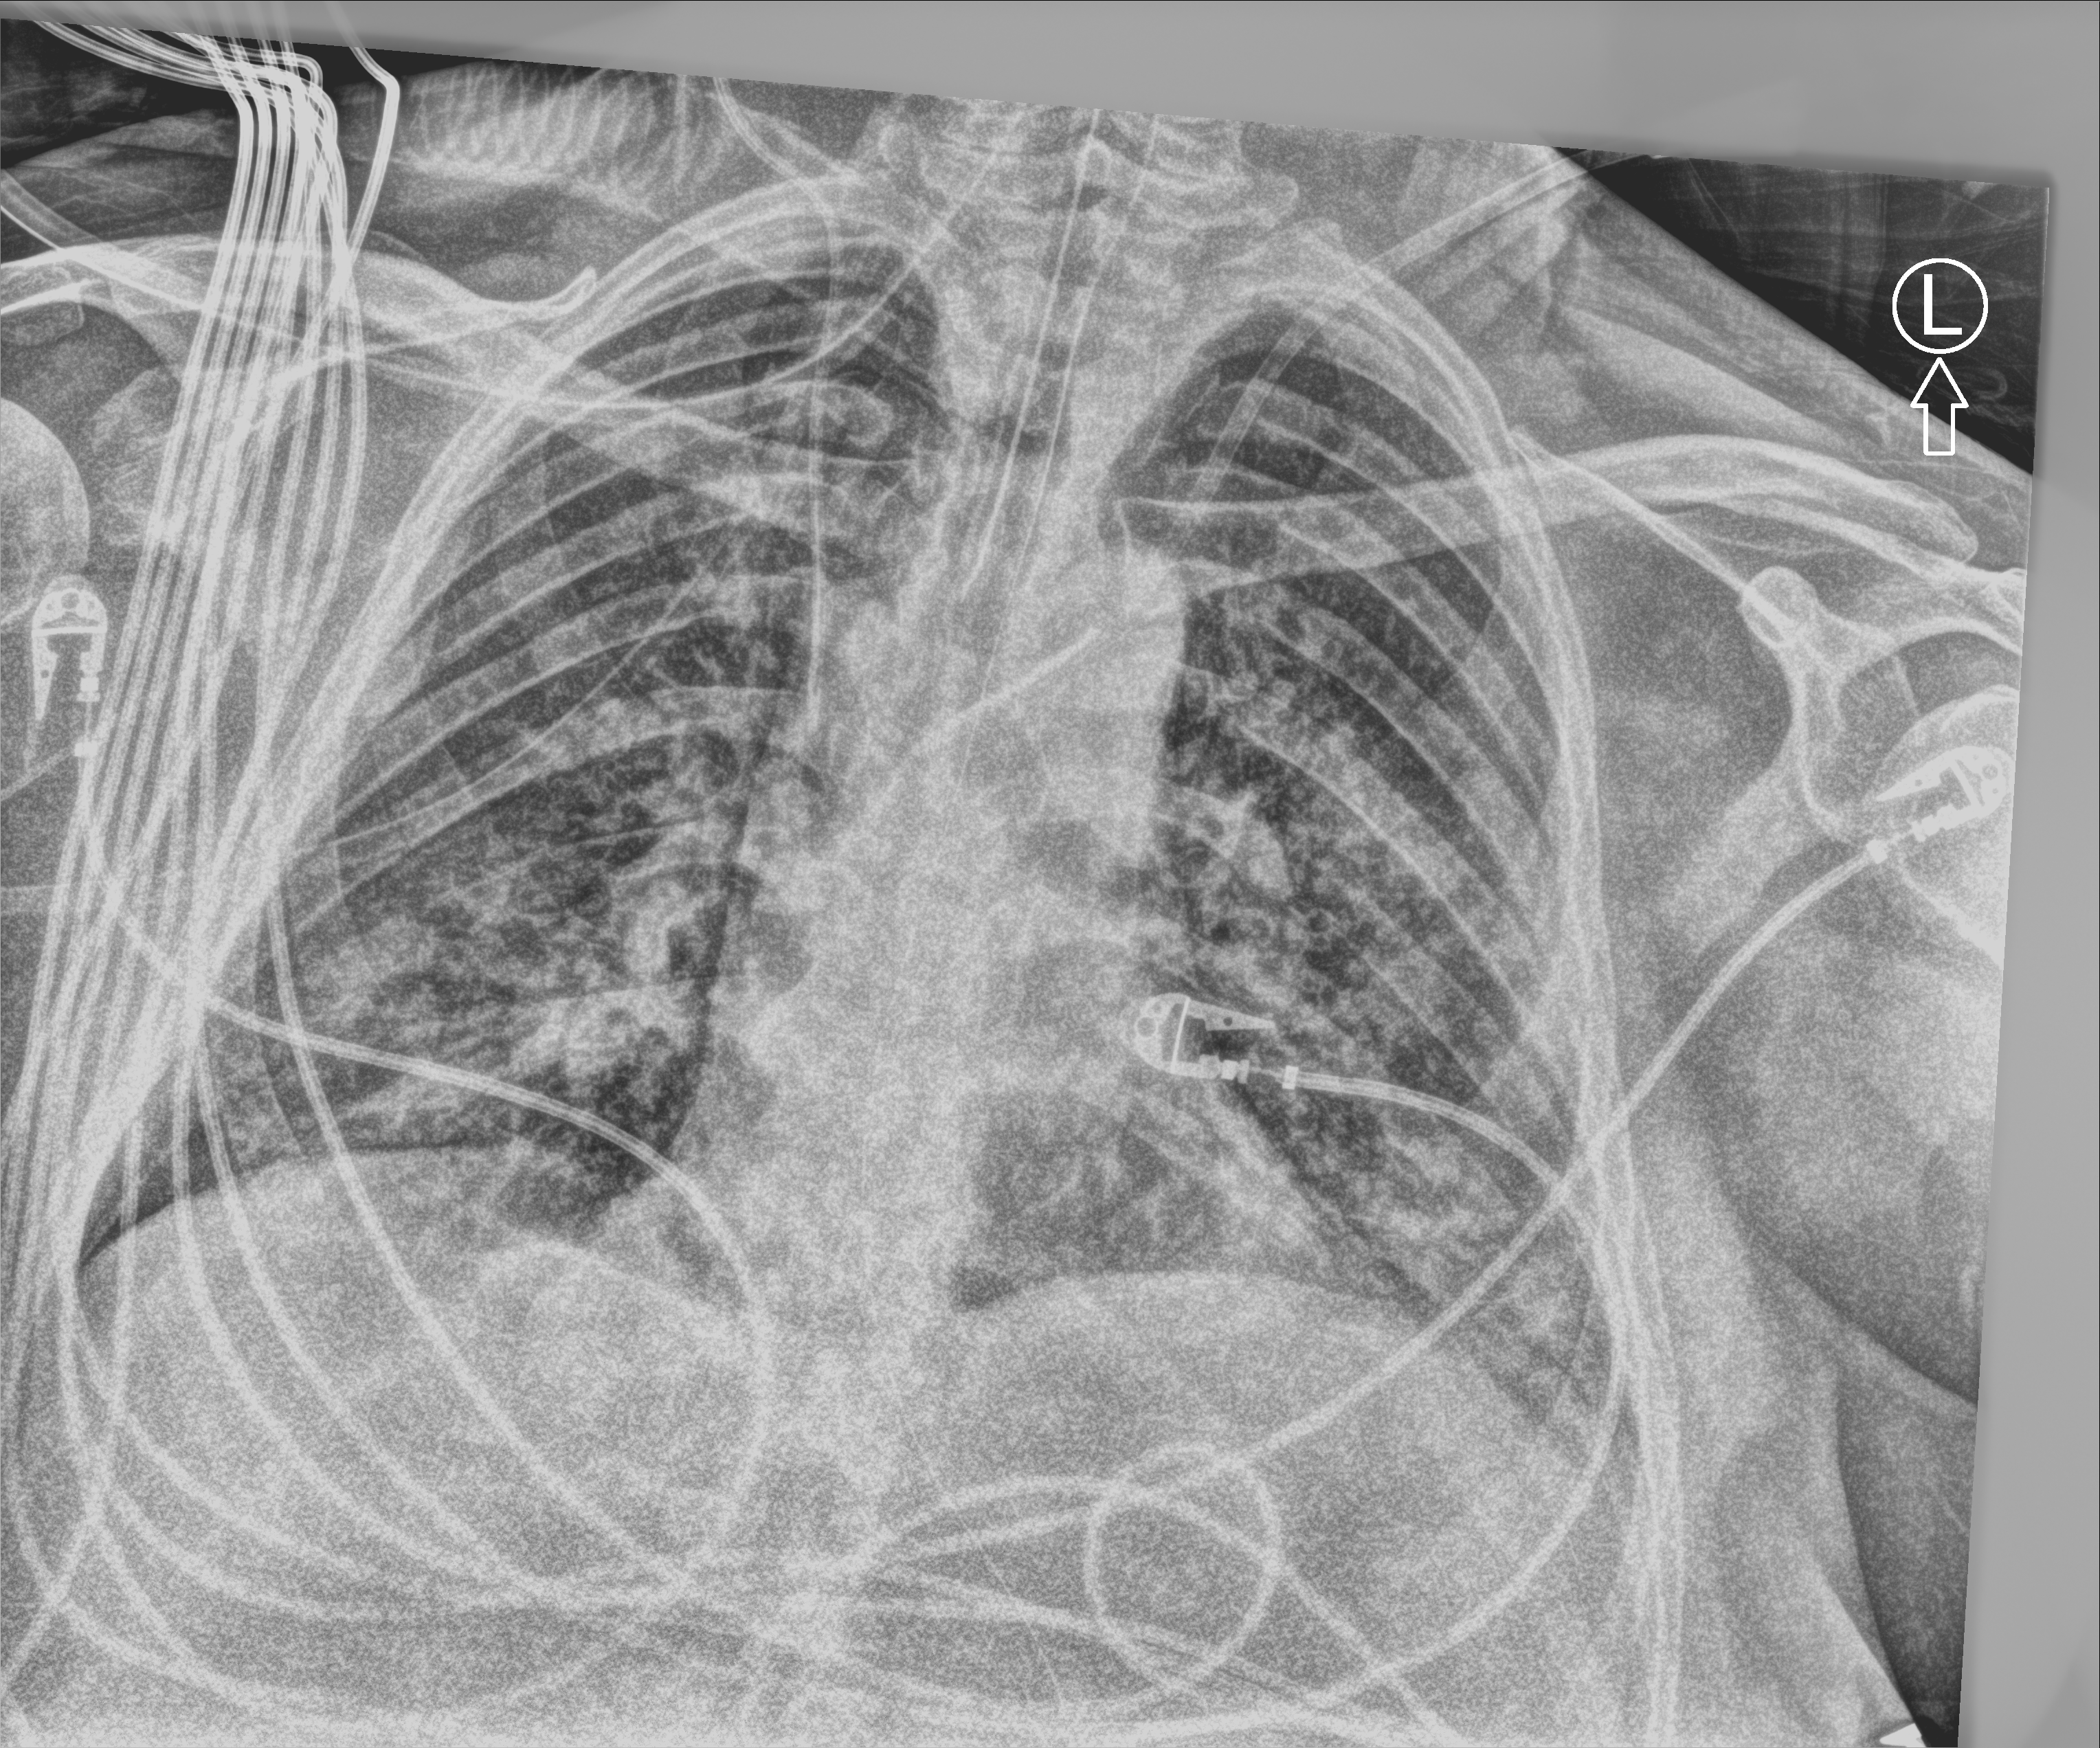
Portable chest radiograph. Patient hospitalised with COVID-19; male, aged 18–59 years.
From the hospital-stay record, not from the radiograph (when in the stay this image was taken is not recorded): length of hospital stay: 39 days; mechanically ventilated during this hospital stay: yes.